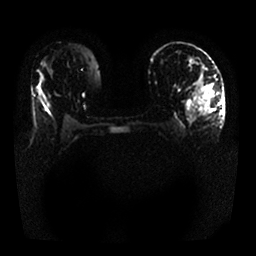
Breast MRI, one axial slice. Position 16 of 25 along the scan axis. Diffusion-weighted series; image 2 of 4 stored at this slice position (different b-values; order by instance number). 1.5 T. 4 mm slice thickness. 256 × 256 image matrix. Female patient.
Outlined on this slice (manually delineated by an expert):
- tumour on diffusion-weighted imaging: bounding box <199,85,214,109> (left, top, right, bottom; pixels)